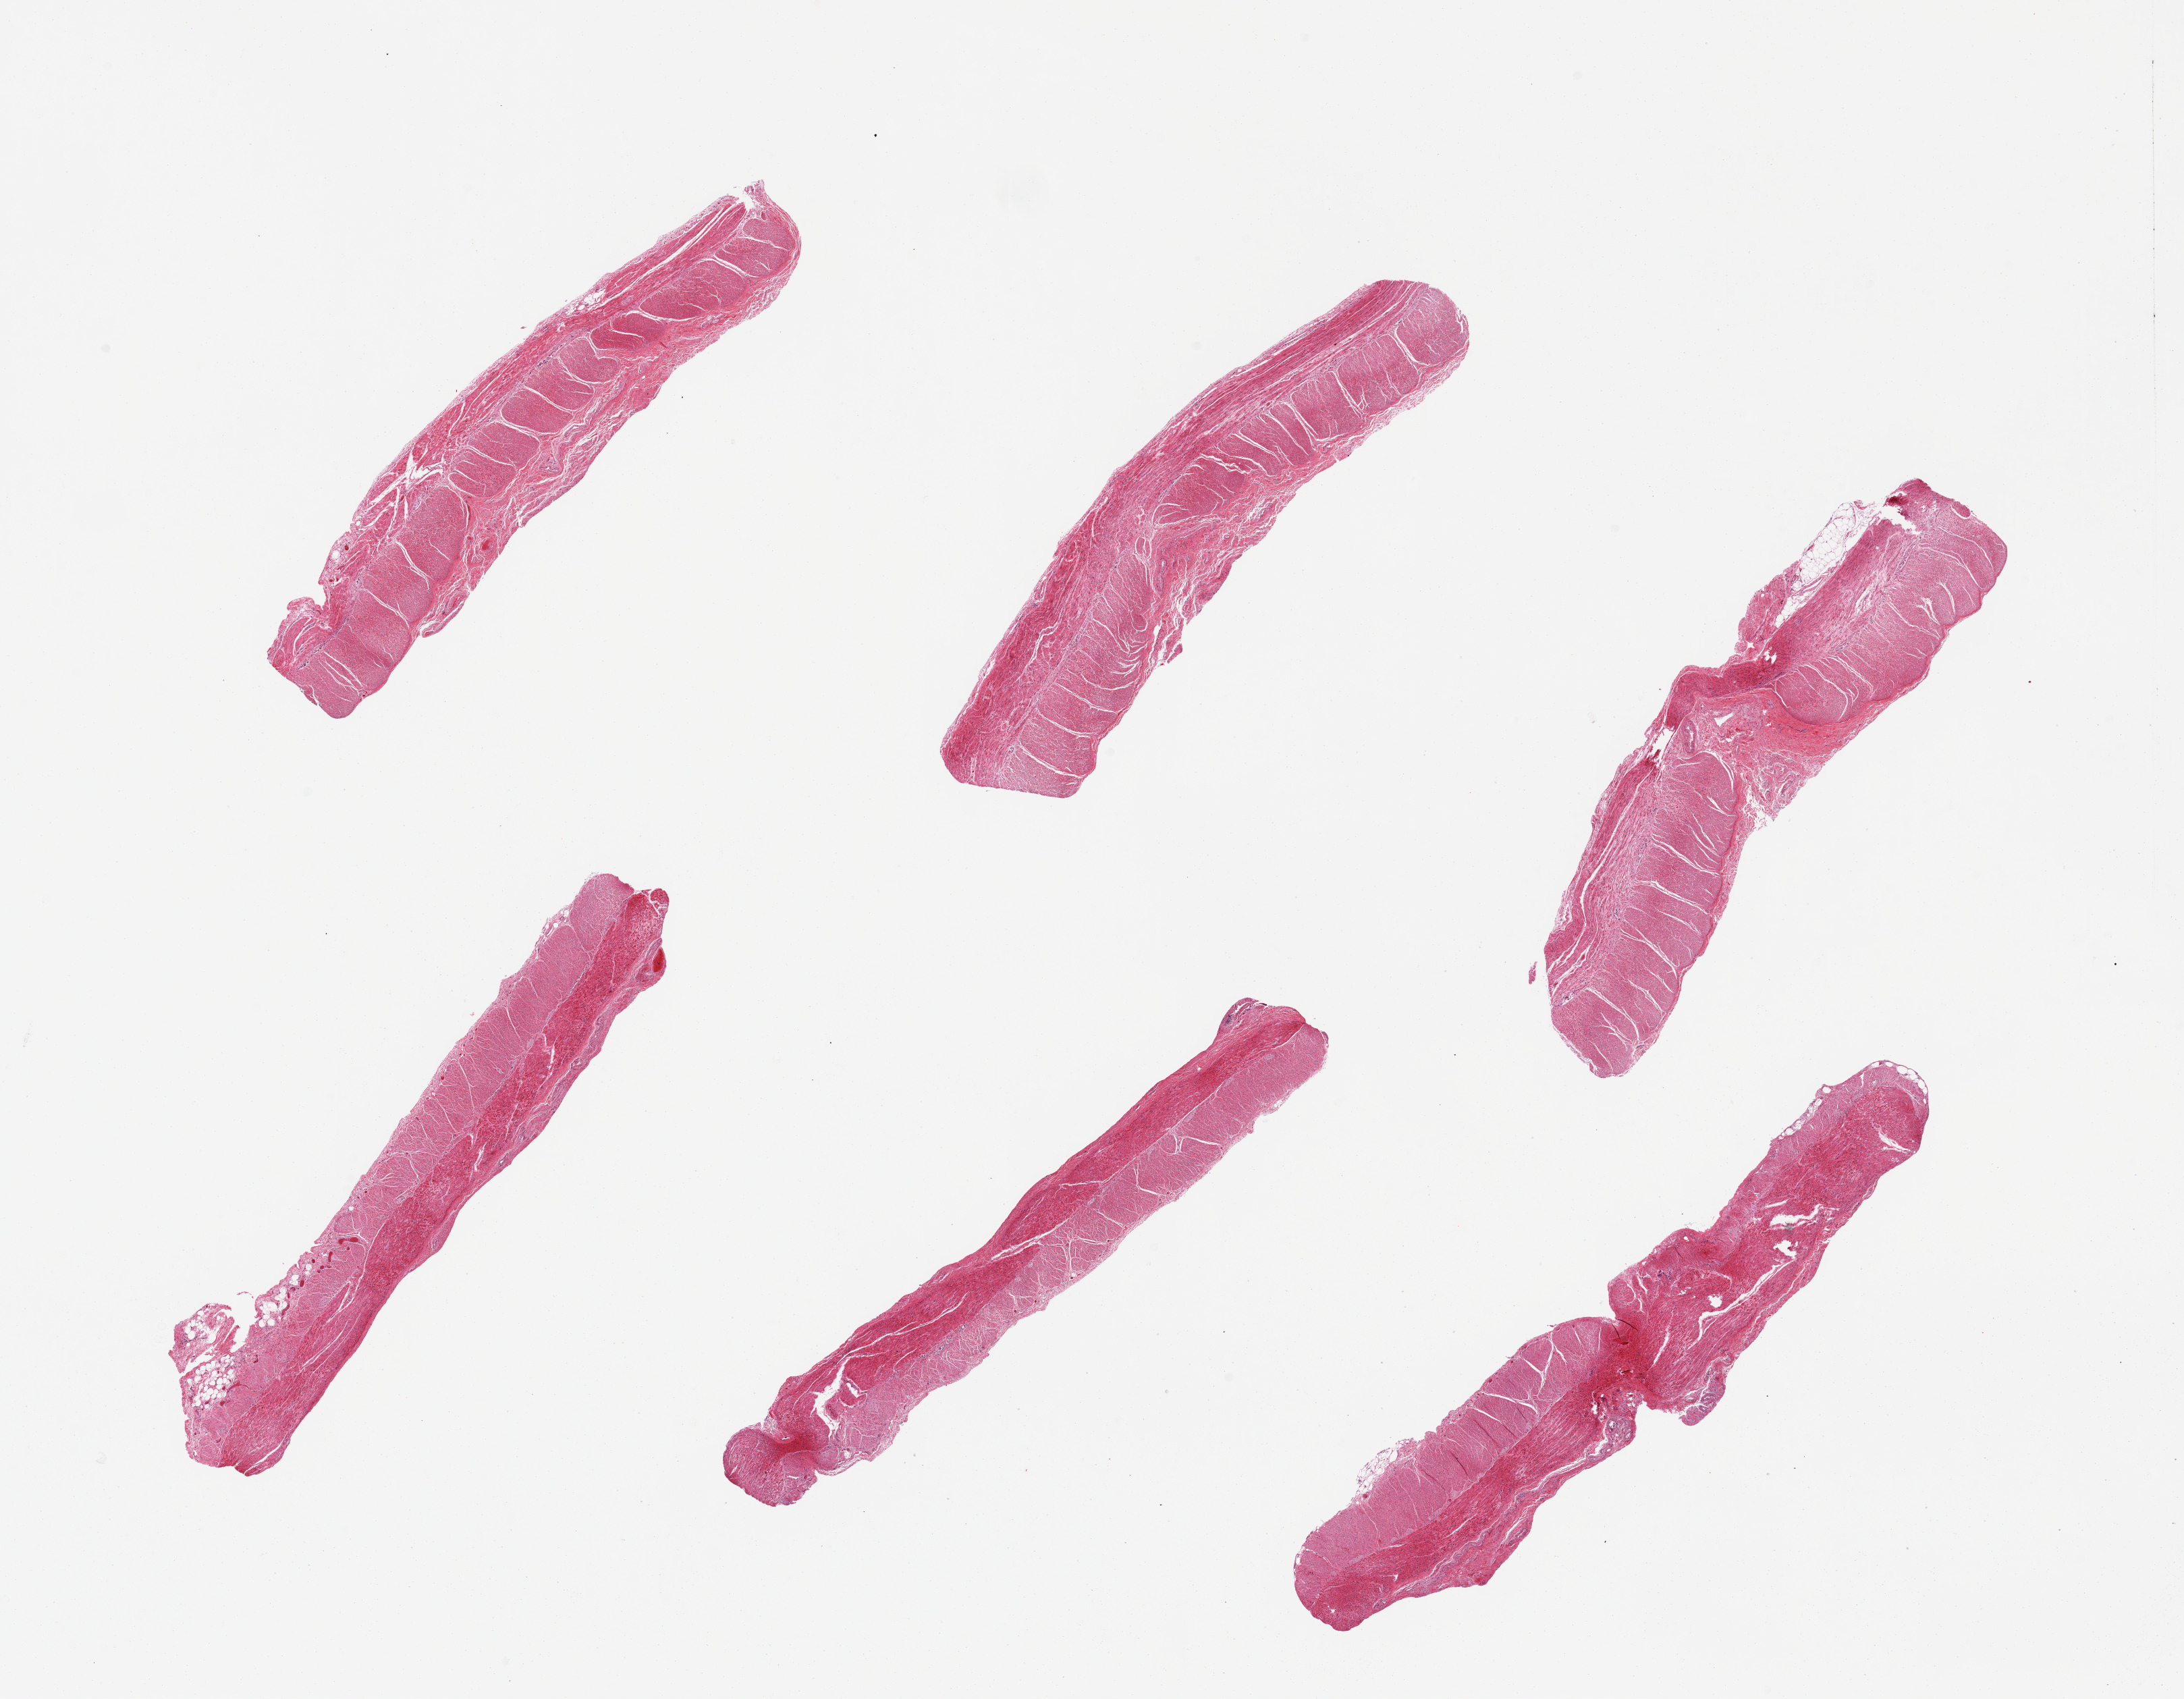
Digitized hematoxylin and eosin (H&E)-stained section, shown as a low-resolution overview of the whole scanned area (about 25.6 x 19.9 mm), PAXgene-fixed, paraffin-embedded tissue, section of sigmoid colon (target tissue), donor tissue sample. Donor sex: female.
• pathologist's review note for this sample: 6 pieces; well dissected muscle